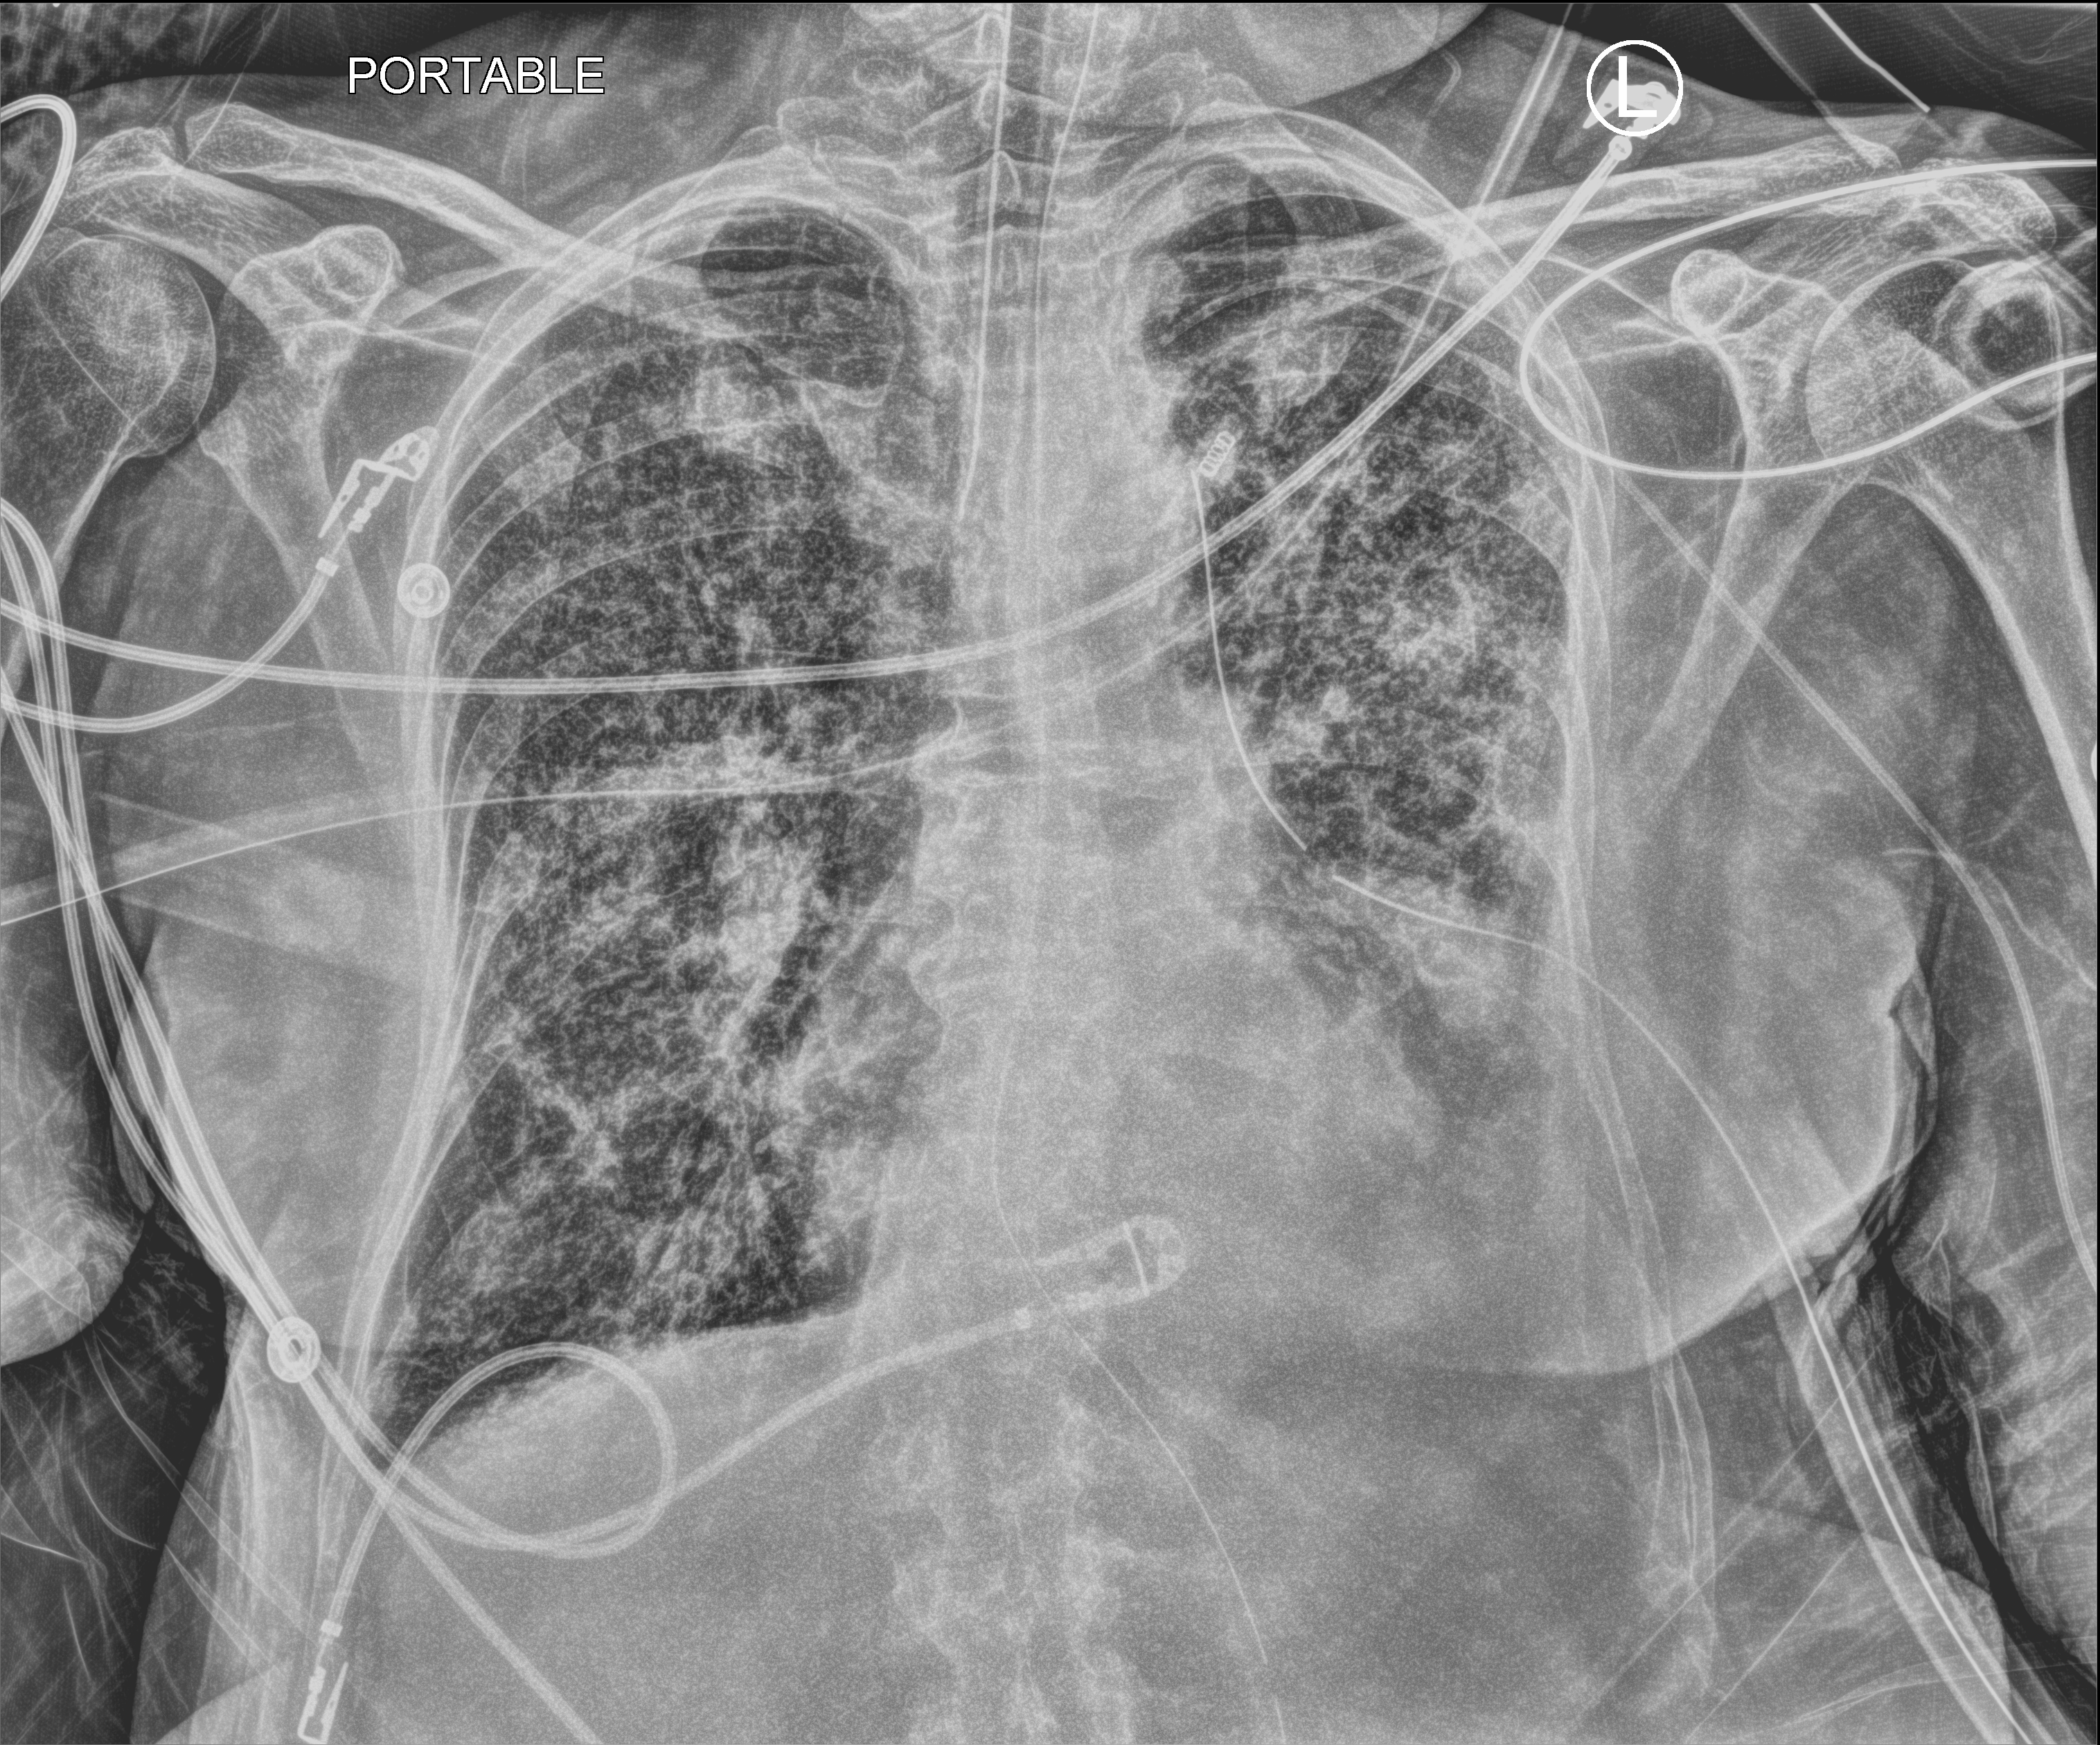
Bedside chest radiograph (computed radiography). Patient hospitalised with COVID-19; female, aged 75–90 years.
Hospital-stay facts (about this admission, not read from this image; timing relative to this image not recorded):
- other chronic lung disease (admission record): yes
- admitted to intensive care during this hospital stay: yes